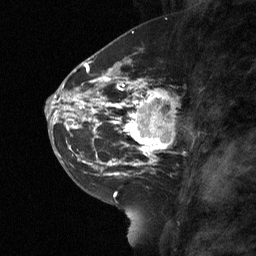
Breast MRI (dynamic contrast-enhanced), one sagittal slice; slice 30 of 64 in the series (ordered by position); dynamic contrast-enhanced study with each time point stored as its own series, time point 2 of 3 at this slice position (early post-contrast, ordered by acquisition time); 1.5 T; TE 4.8 ms, TR 27 ms; 256 × 256 image matrix, field of view 180 × 180 mm. Patient: female, 42 years. Case-level facts recorded for this patient, not image findings: setting: breast cancer imaged before/during neoadjuvant chemotherapy; receptor status: triple-negative.
Annotated regions visible in this slice (semi-automatically segmented with operator editing):
- analysis volume of interest (the breast-tissue region the enhancement analysis was run in; not a lesion): bounding box [x1, y1, x2, y2] px = [115, 85, 176, 160]
- tumour enhancement mask (voxels above the 90 % enhancement threshold inside the analysis volume of interest): [115, 85, 170, 160]